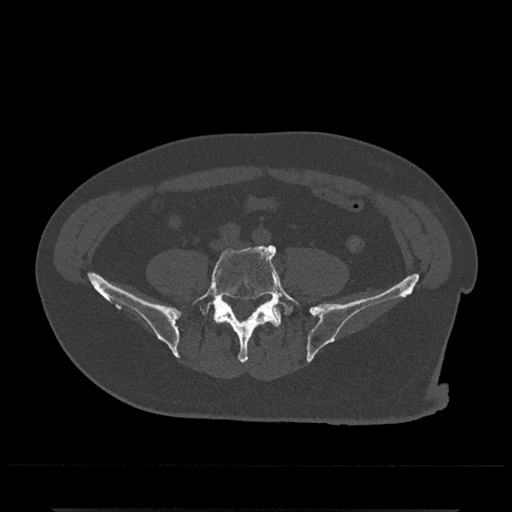
CT including the spine, one axial slice; position 85 of 797 along the scan axis; reconstruction kernel Br40s/3; bone window (W 1800 / L 400 HU); 512 × 512 image matrix, field of view 393 × 393 mm. Male patient, age 67 years. From the clinical record (not read from this slice): primary cancer: prostate.
Outlined on this slice (semi-automatic segmentation, software-assisted and operator-edited):
- L5 vertebra: bounding box (x1, y1, x2, y2) in pixels: (192, 245, 301, 363)